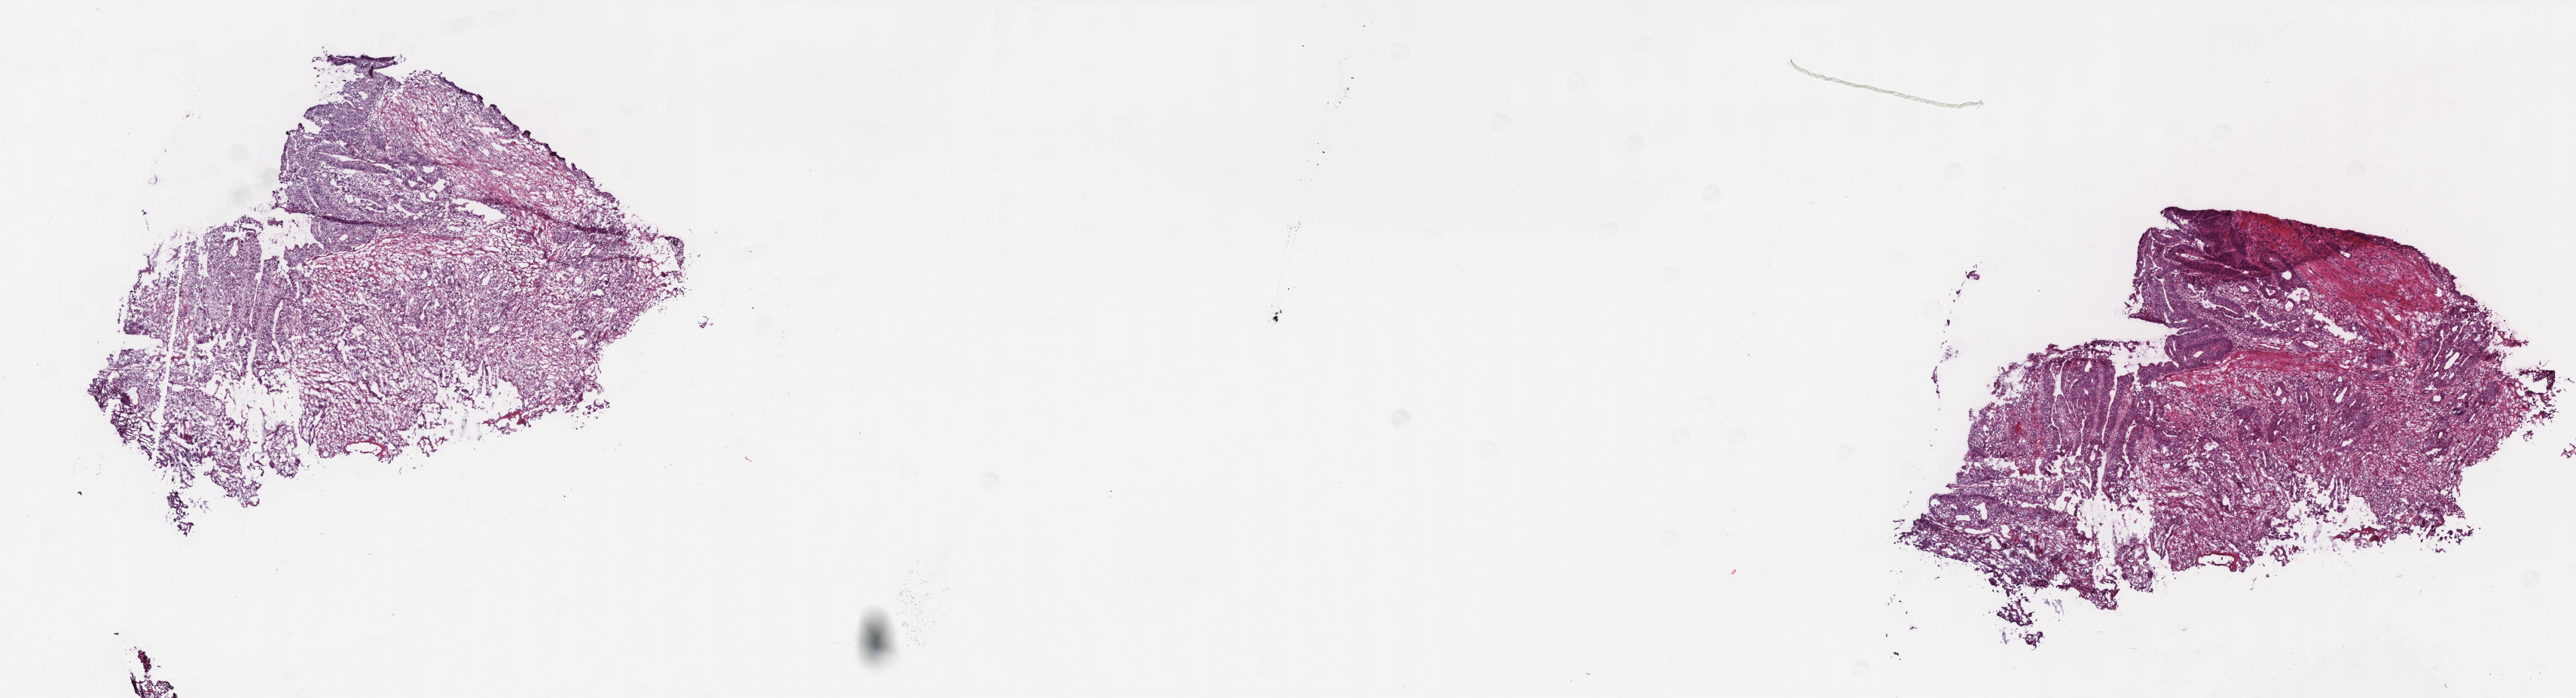
H&E whole-slide image, shown as a low-resolution overview of the whole scanned area (about 13.7 x 3.7 mm, from a 40x scan), frozen section, sample: primary tumour, colon. Female patient; age at initial diagnosis 66 years. Pathologist review of this section (percent, as recorded): tumour cells 75%, tumour nuclei 75%, normal cells 0%, stromal cells 23%, necrosis 2%. Infiltration values recorded for this section: lymphocyte infiltration 13%, monocyte infiltration 6%, neutrophil infiltration 2%.
- AJCC pathologic stage: IIIB
- histologic diagnosis: Adenocarcinoma, NOS (sigmoid colon)